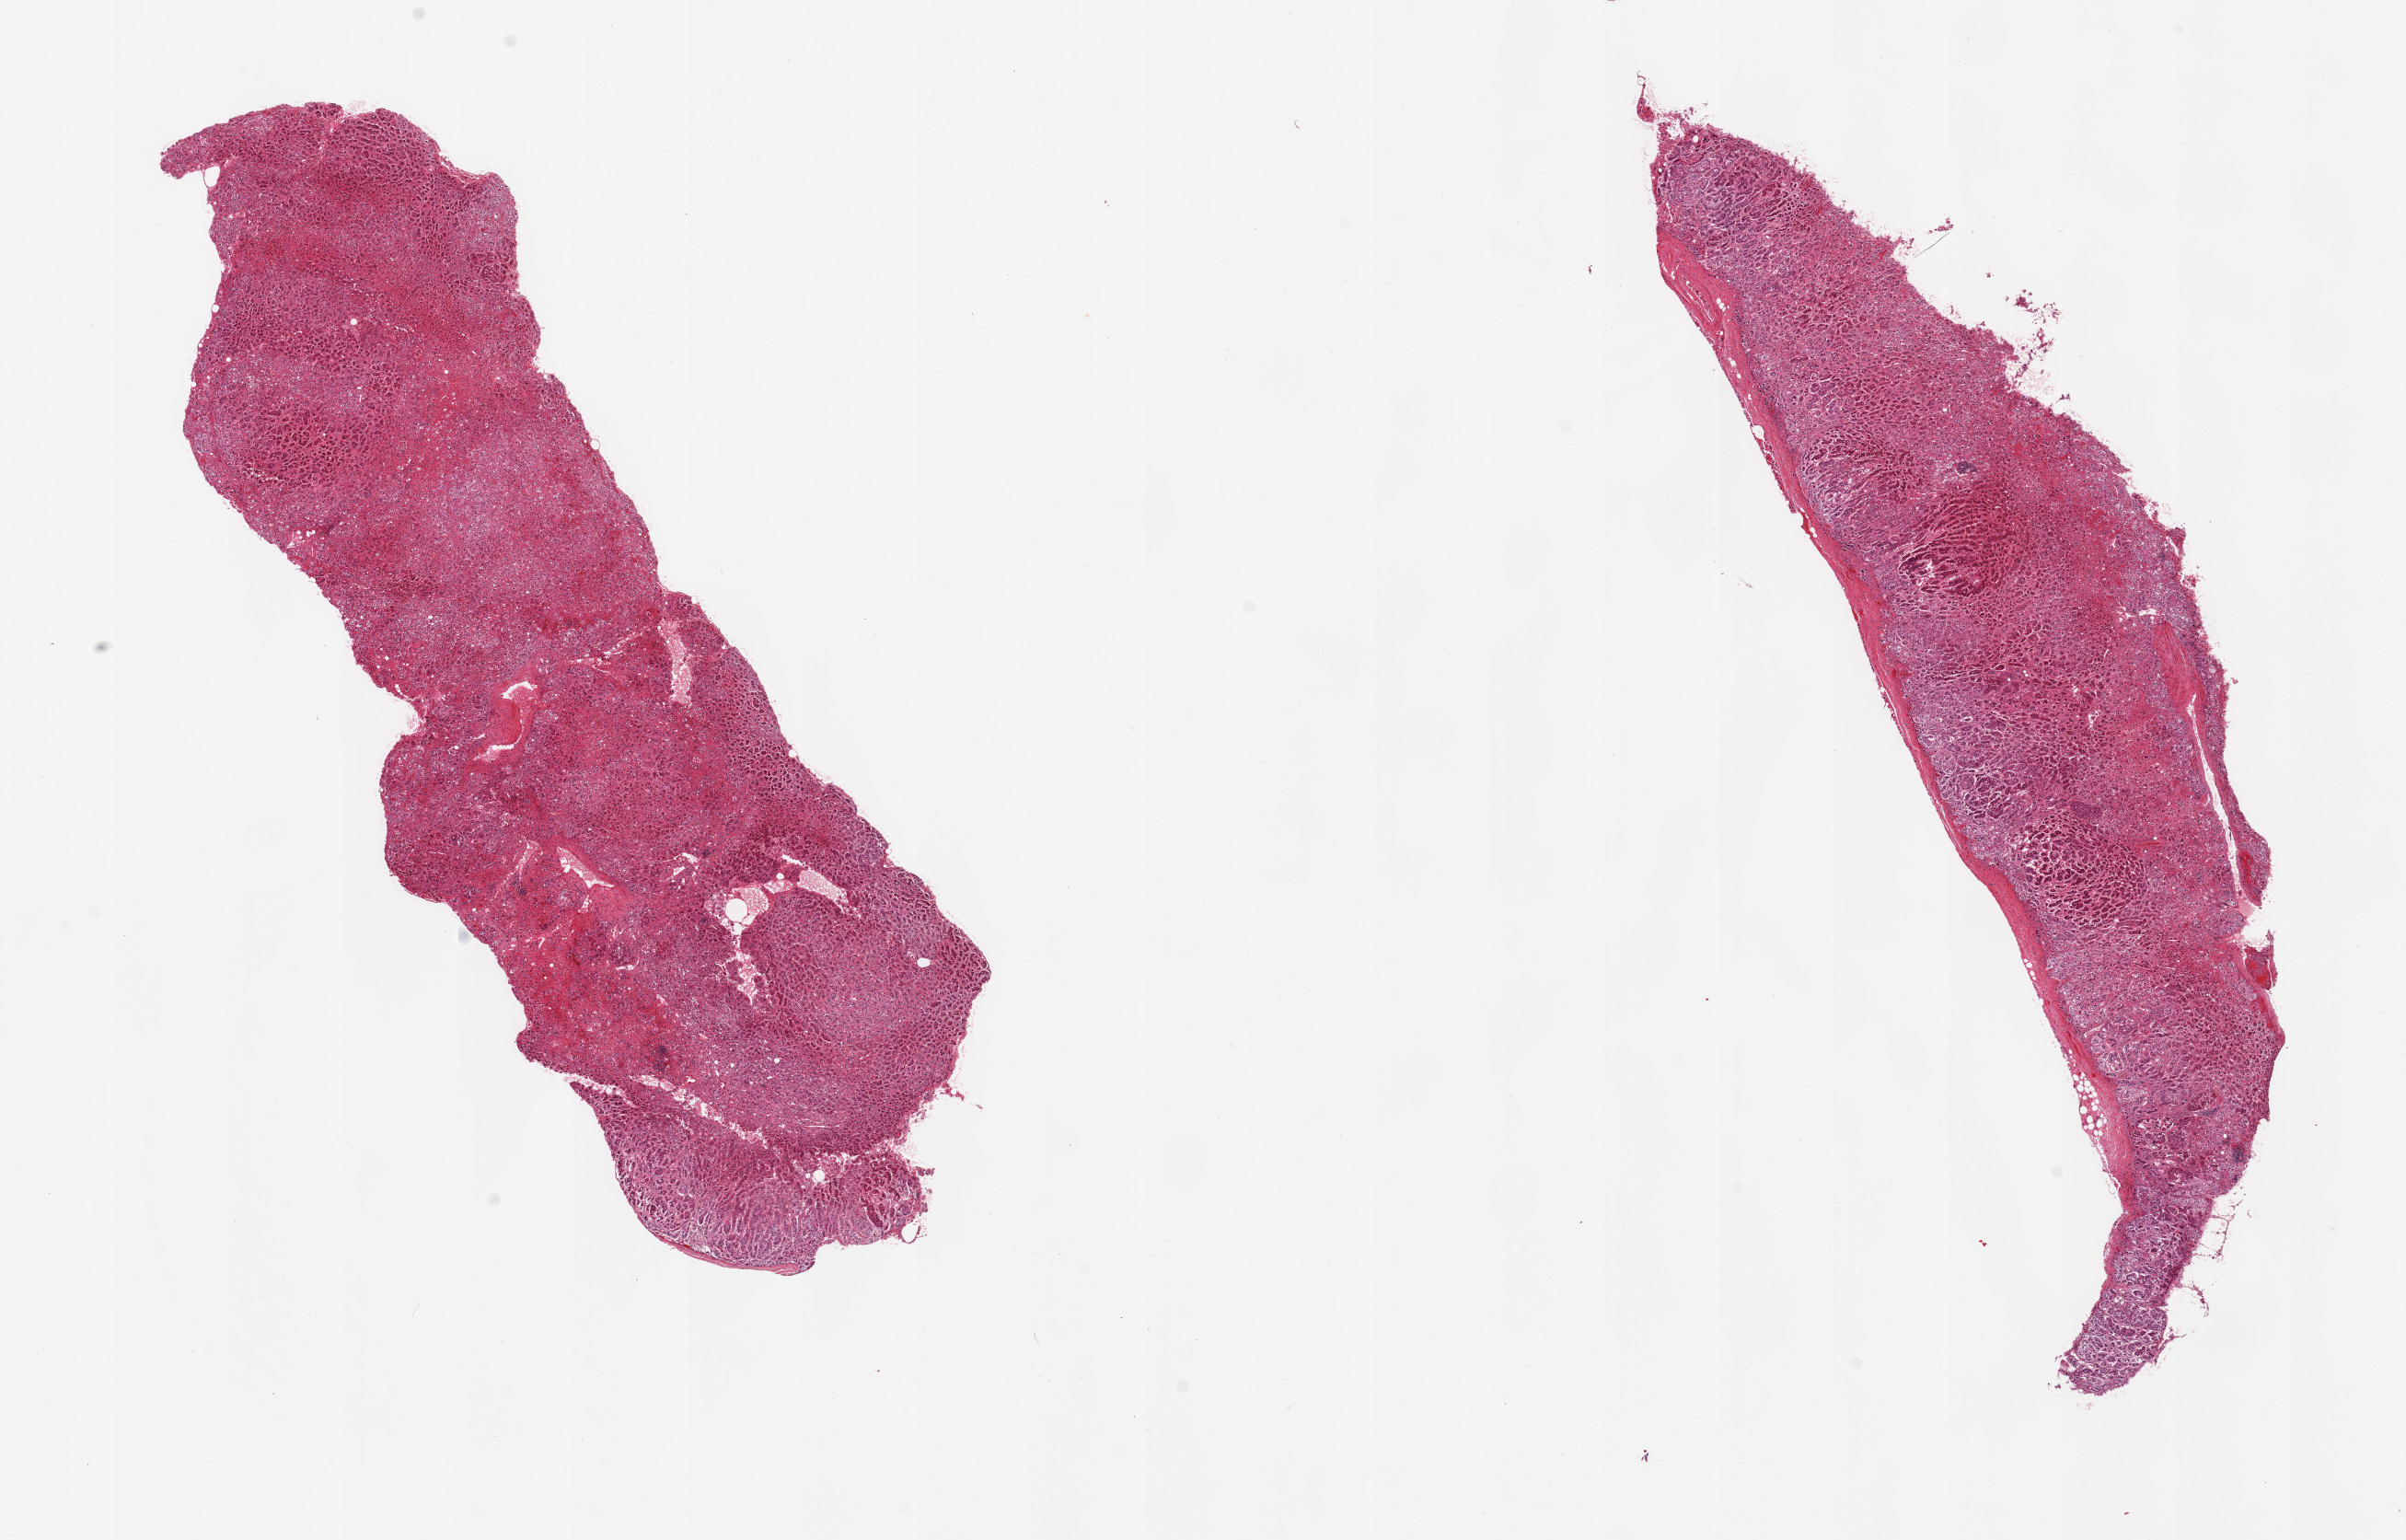
Digitized H&E-stained section — a low-resolution overview of the entire scanned area, about 20.7 x 13.2 mm; PAXgene-fixed paraffin-embedded (PFPE) section; sampled site (target tissue): adrenal gland; donor tissue sample. Donor: male.
- reviewer comment on this tissue sample: 2 pieces, essentially all cortex but autolysis far advanced